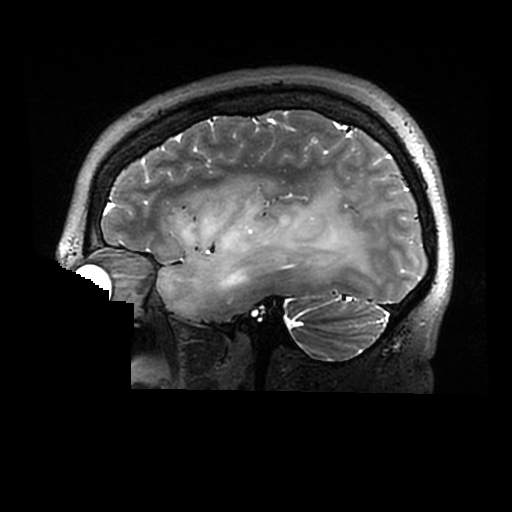
Brain MRI from a brain-tumour surgery series, one sagittal slice. Position 214 of 320 along the scan axis. 0.6 mm slice thickness. 512 × 512 image matrix. From the clinical record (not read from this slice): histopathology: Astrocytoma; WHO grade: 2; IDH mutation: yes.
Structures marked on this image (outlined manually by an expert reader):
- tumour: bounding box [x1, y1, x2, y2] px = [157, 185, 376, 314]